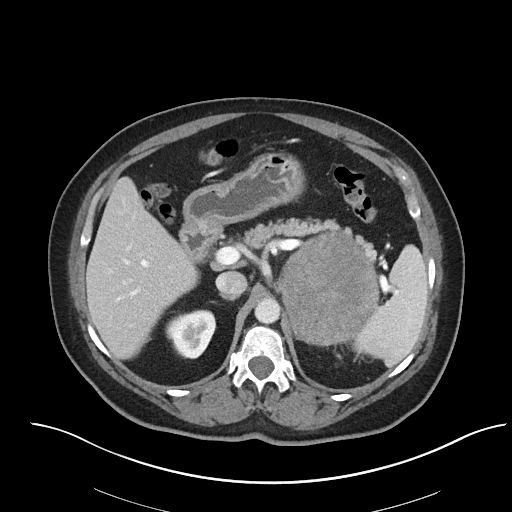
Contrast-enhanced abdominal CT, one axial slice; position 51 of 92 along the scan axis; 120 kVp; intravenous contrast given; soft-tissue window (W 400 / L 40 HU); 512 × 512 image matrix, field of view 440 × 440 mm. Patient: female, 53 years. From the clinical record (not read from this slice): diagnosis: adrenocortical carcinoma; tumour side: left adrenal; tumour size at pathology: 9 cm; Ki-67 index: 28 %; stage (as recorded): 2.
Outlined on this slice (semi-automatic segmentation, software-assisted and operator-edited):
- mass: box from (x=282, y=234) to (x=377, y=344) px